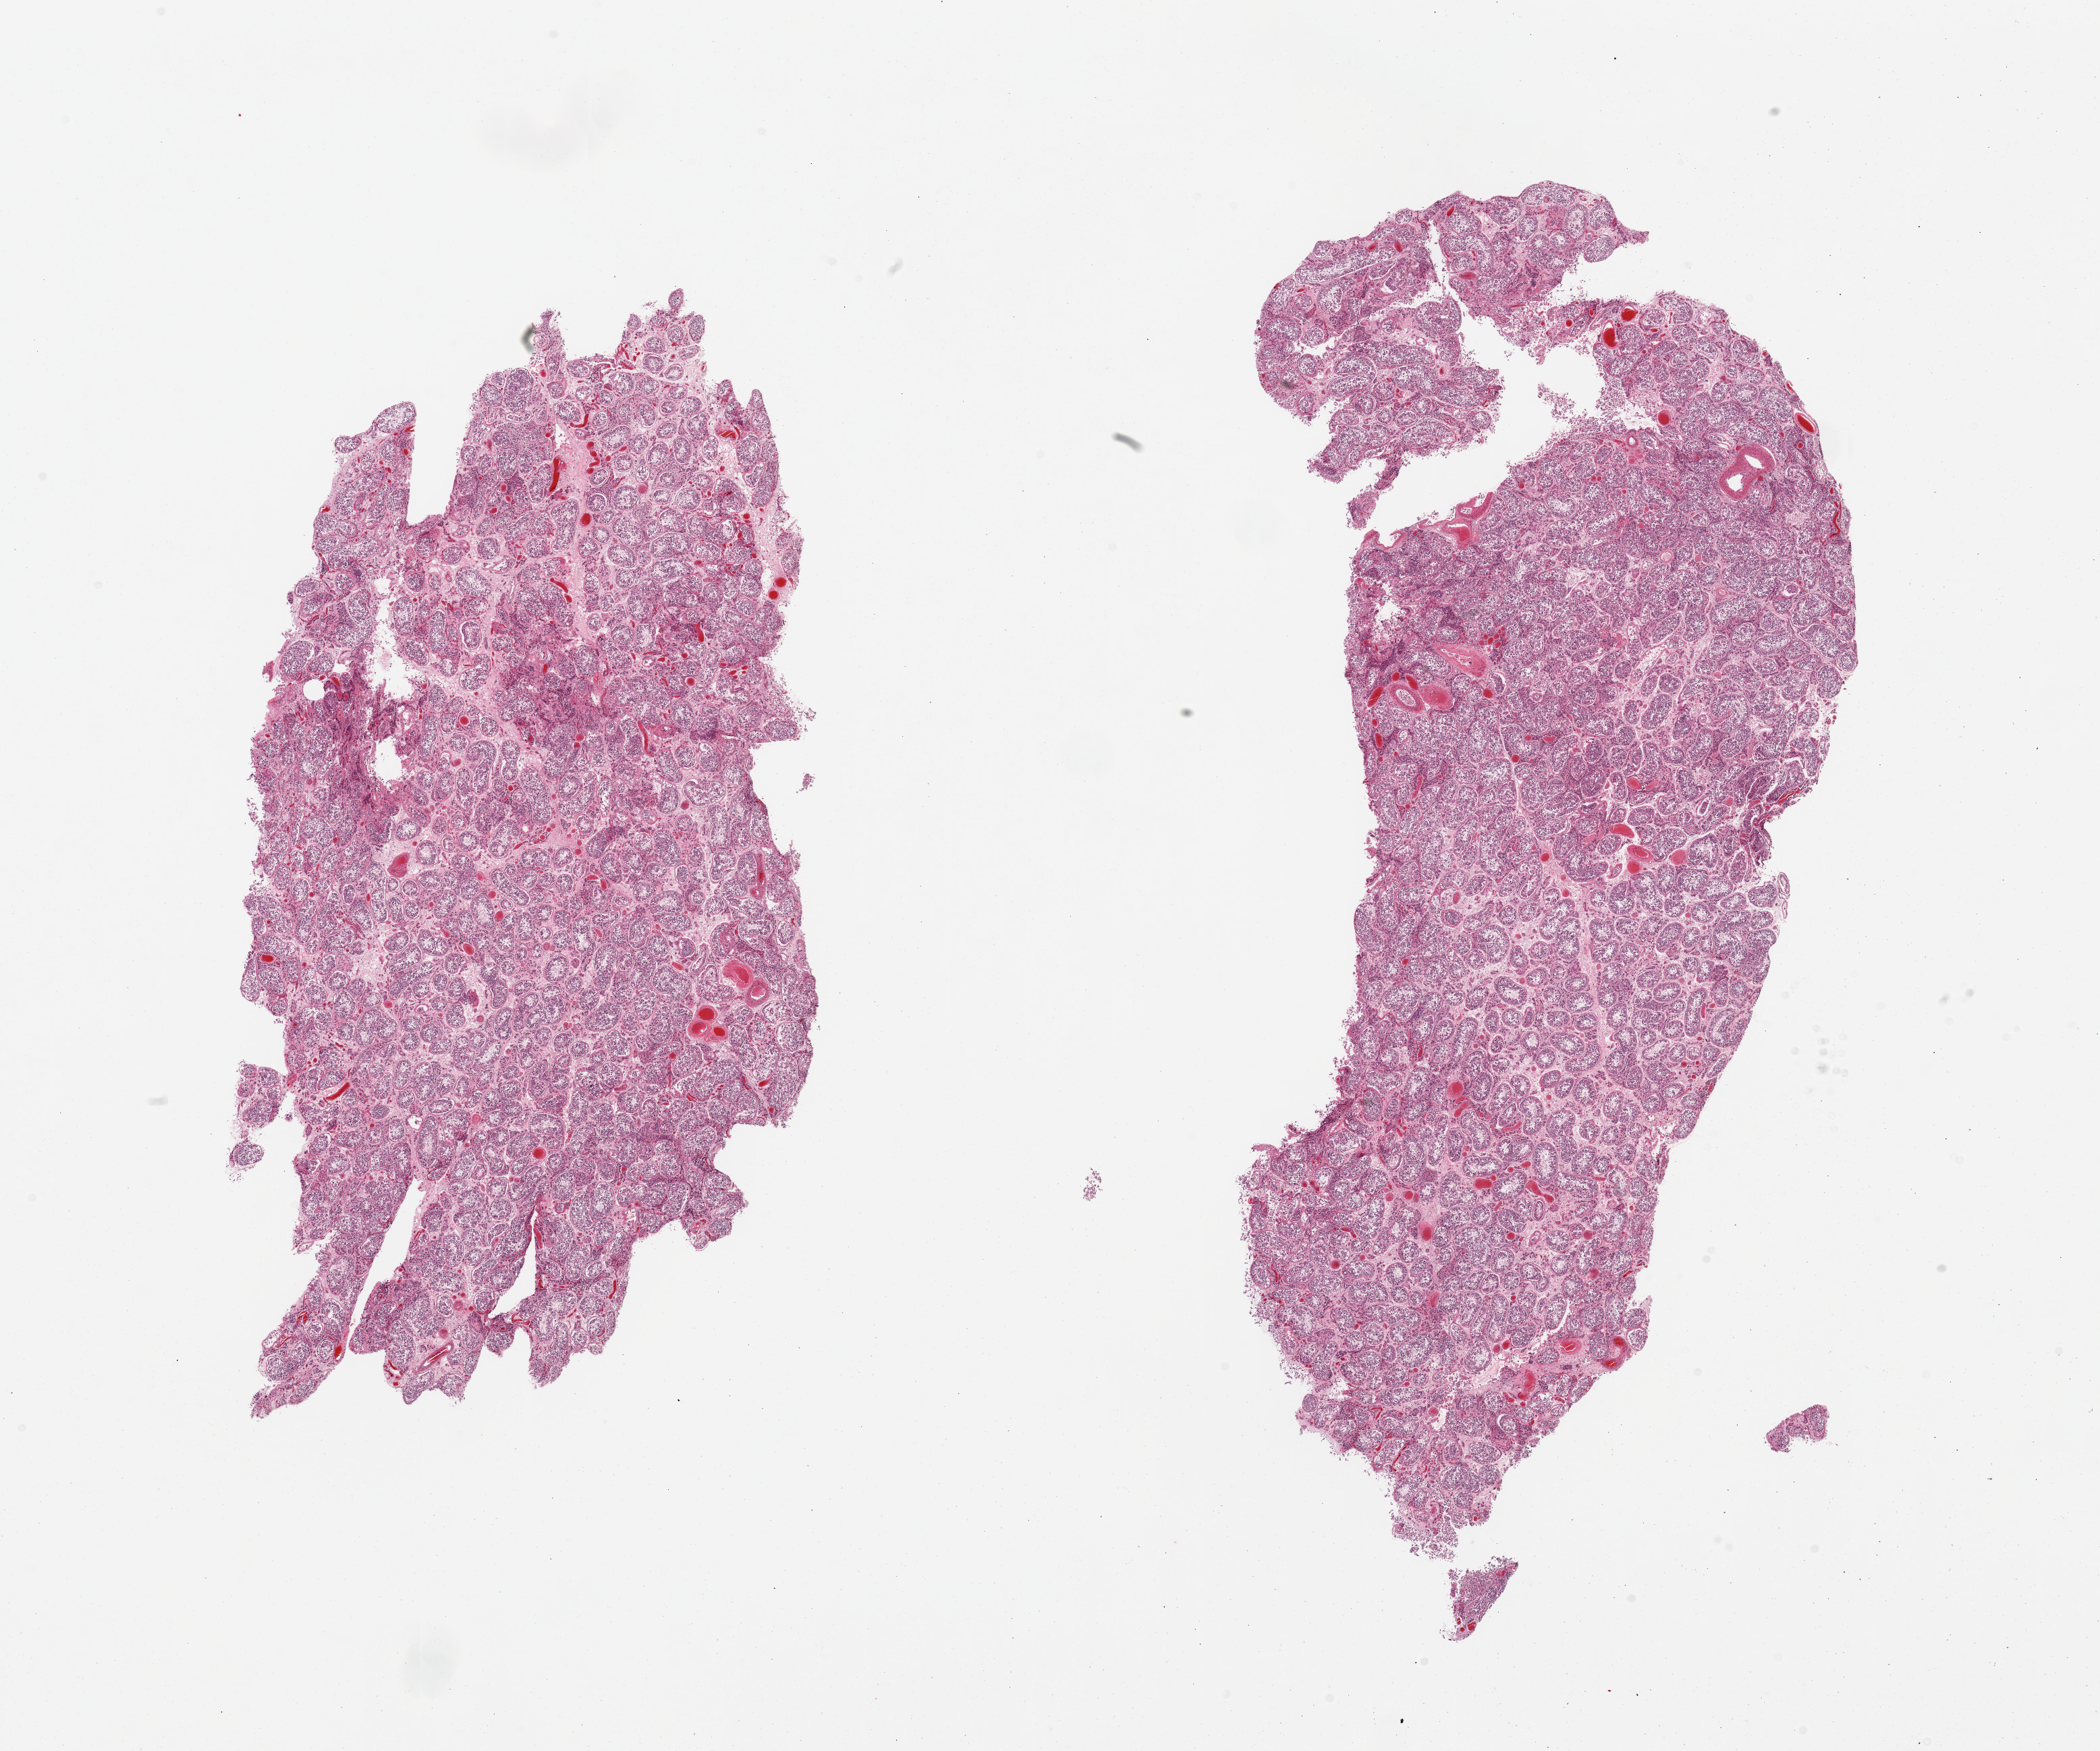
Digitized H&E-stained section, shown as a low-resolution overview of the whole scanned area (about 24.6 x 20.5 mm, acquisition: 20x scan); PAXgene-fixed, paraffin-embedded tissue; target tissue: testis; tissue donor sample. Male donor.
* pathologist's review note for this sample: 2 pieces; spermatogenesis